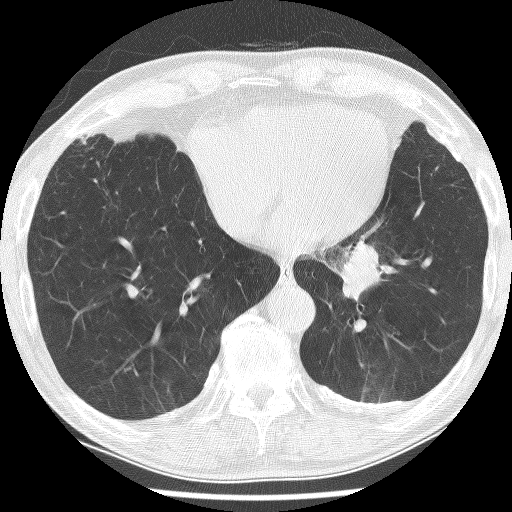
Low-dose screening chest CT, one axial slice; 120 kVp; lung window (W 1500 / L -600 HU); 512 × 512 image matrix.
Outlined on this slice (expert manual segmentation):
- lesion 1 (tumor, lower lobe of left lung): bounding box <341,240,380,302> (left, top, right, bottom; pixels)